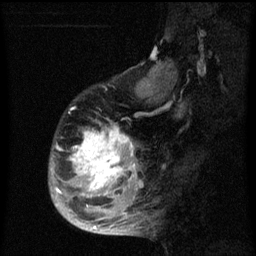
Breast MRI (dynamic contrast-enhanced), one sagittal slice; position 20 of 60 along the scan axis; dynamic contrast-enhanced series, image 2 of 3 at this slice position (ordered by acquisition); 1.5 T; TE 4.2 ms, TR 8 ms; 2 mm slice thickness; 256 × 256 image matrix, field of view 190 × 190 mm. Female patient, age 50 years.
Structures marked on this image (semi-automatic segmentation, software-assisted and operator-edited):
- analysis volume of interest (the breast-tissue region the enhancement analysis was run in; not a lesion): bounding box (x1, y1, x2, y2) in pixels: (49, 90, 142, 216)
- tumour enhancement mask (voxels above the 70 % enhancement threshold inside the analysis volume of interest): (56, 126, 137, 208)